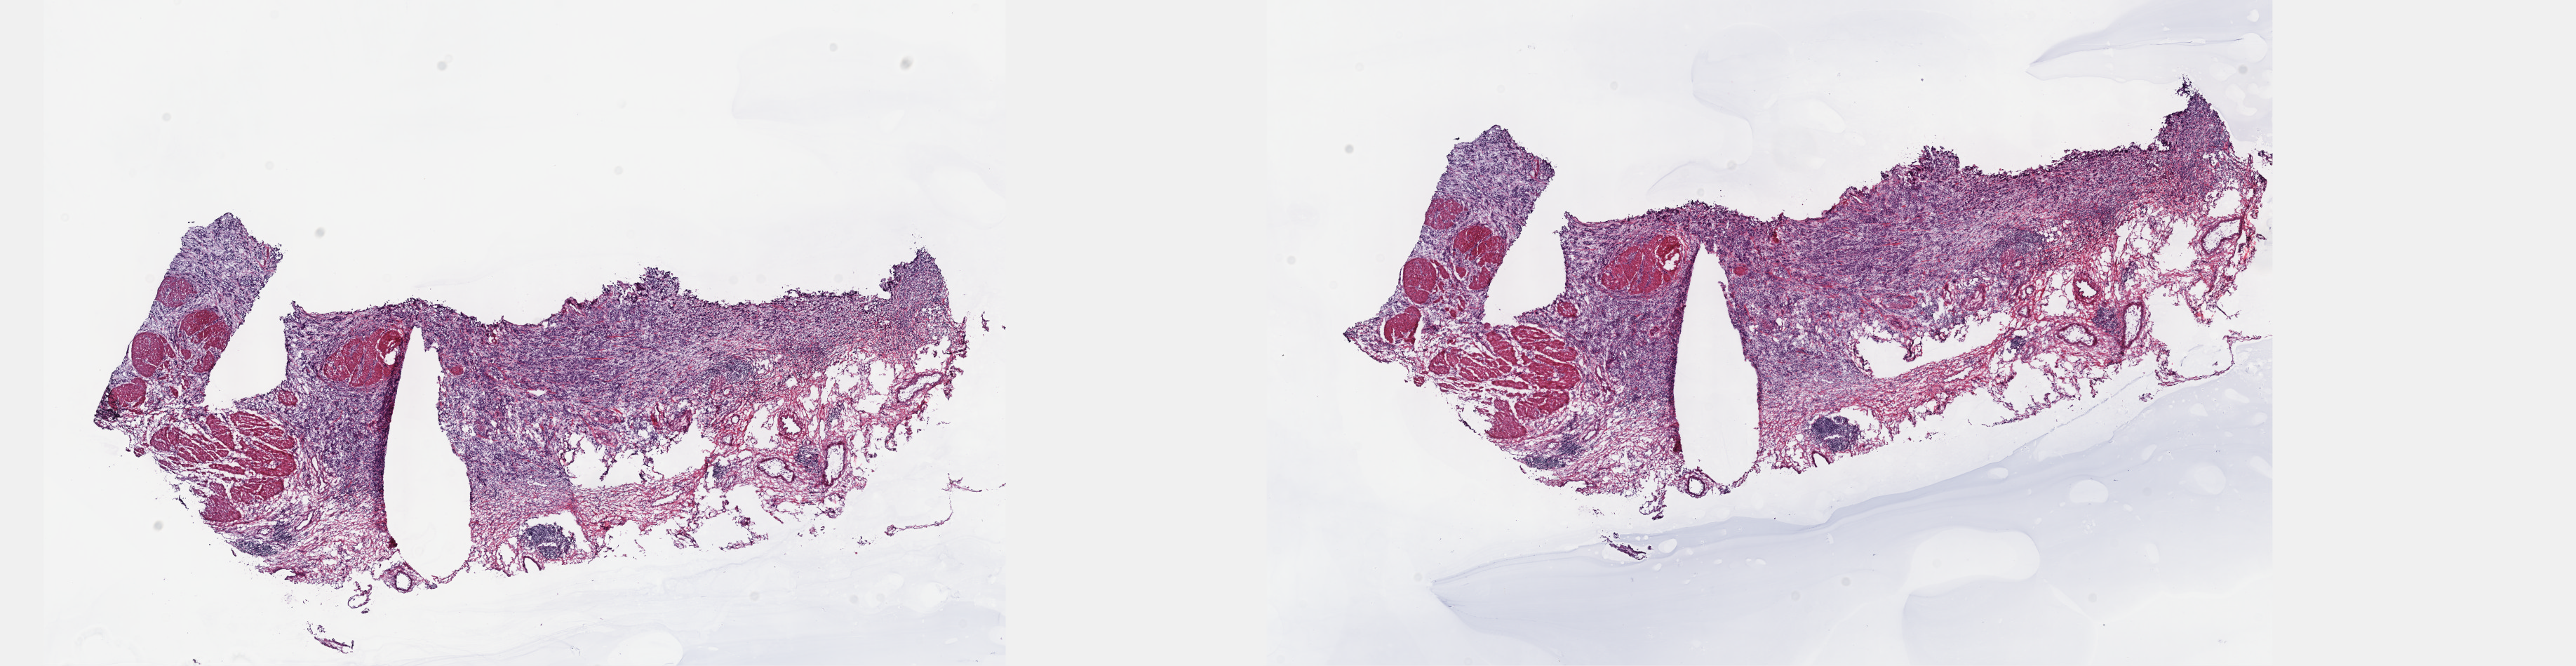
Digitized H&E-stained tissue section (whole slide) — low-resolution overview of the scanned area, about 29.7 x 7.7 mm; frozen section from the top of the tissue portion; bladder, primary tumour sample. Patient: female, age at initial diagnosis 69 years. Slide review estimates, as recorded: tumour cells 65%, tumour nuclei 65%.
Histologic diagnosis: Transitional cell carcinoma.